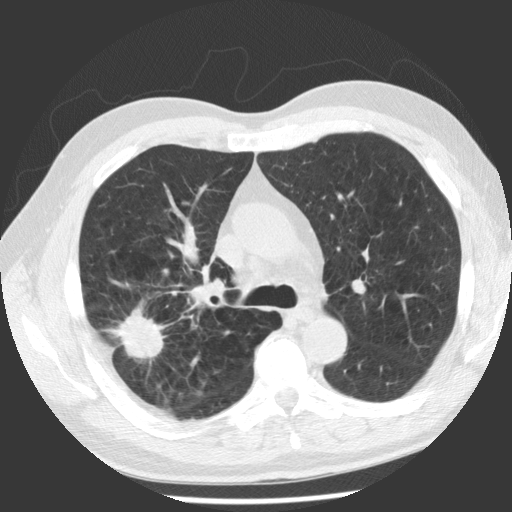
Low-dose screening chest CT, one axial slice. Slice 74 of 112 in the series (ordered by position). Reconstruction kernel STANDARD. Lung window (W 1500 / L -600 HU). 512 × 512 image matrix.
Outlined on this slice (manually delineated by an expert):
- lesion 1 (tumor, upper lobe of right lung): box from (x=118, y=305) to (x=164, y=359) px